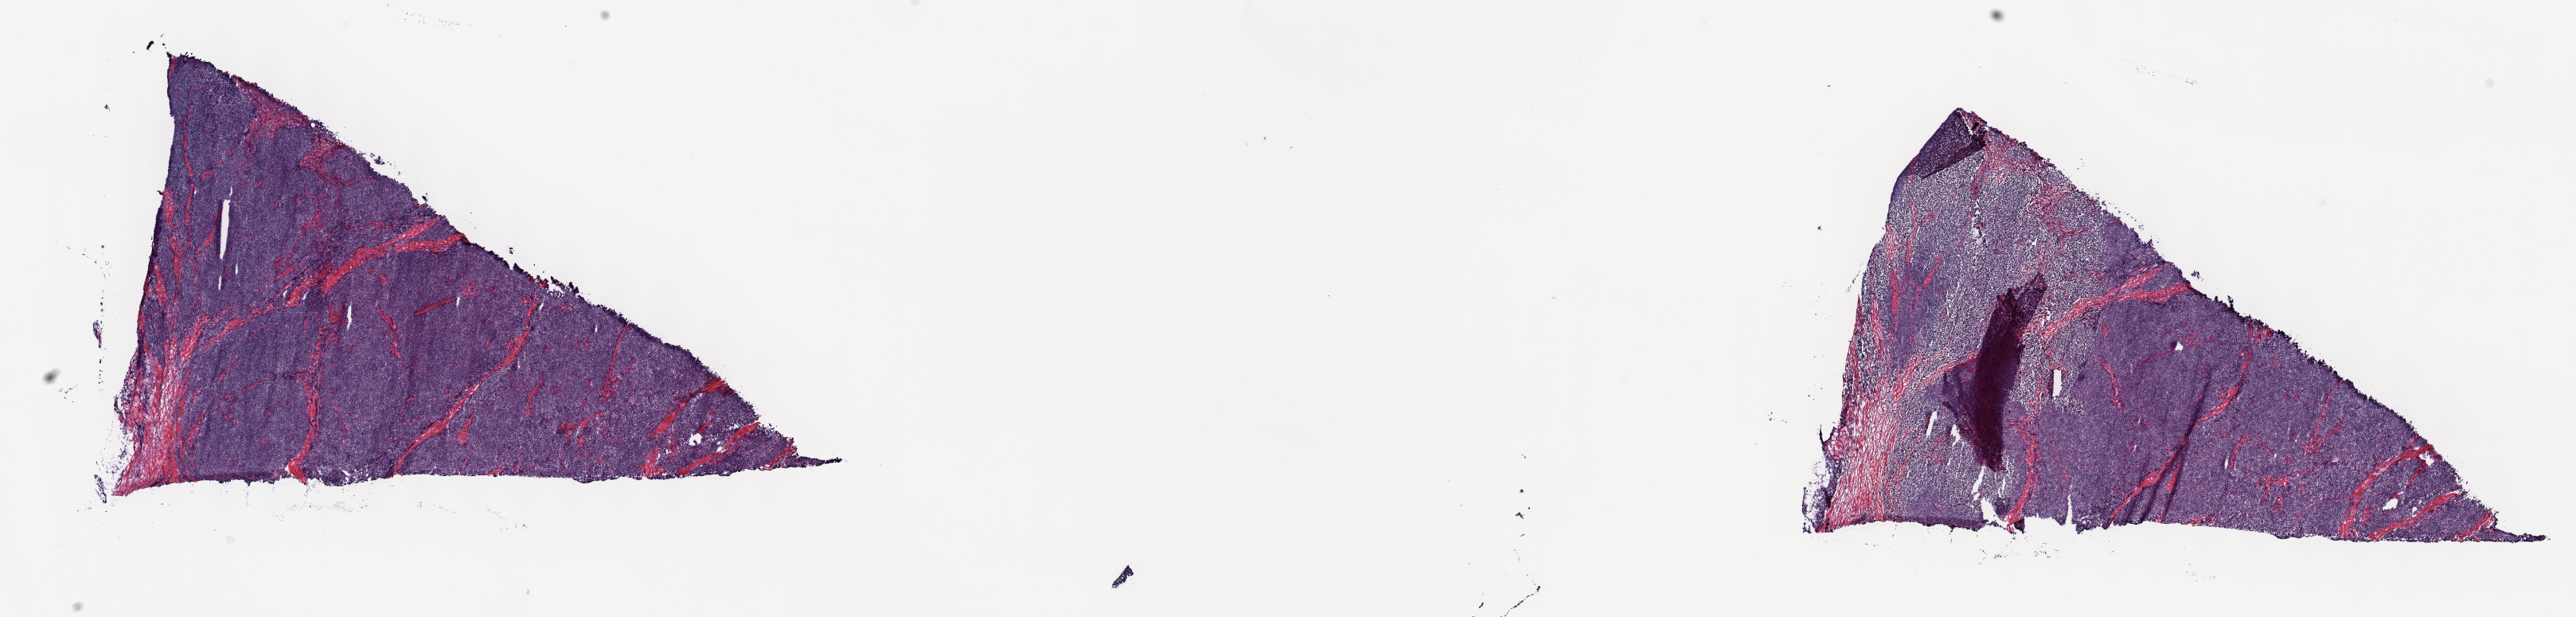
Whole-slide histology image, Hematoxylin and eosin (H&E) stained — a low-resolution overview of the entire scanned area, about 26.2 x 6.3 mm (from a 40x scan), frozen section, primary tumour sample from the thymus. Female, age 60 years at initial diagnosis. Slide review estimates, as recorded: tumour cells 100%, tumour nuclei 80%, normal cells 0%, stromal cells 0%, necrosis 0%. Infiltration values recorded for this section: lymphocyte infiltration 1%, monocyte infiltration 0%, neutrophil infiltration 0%.
- pathologic diagnosis: Thymoma, type B1, malignant